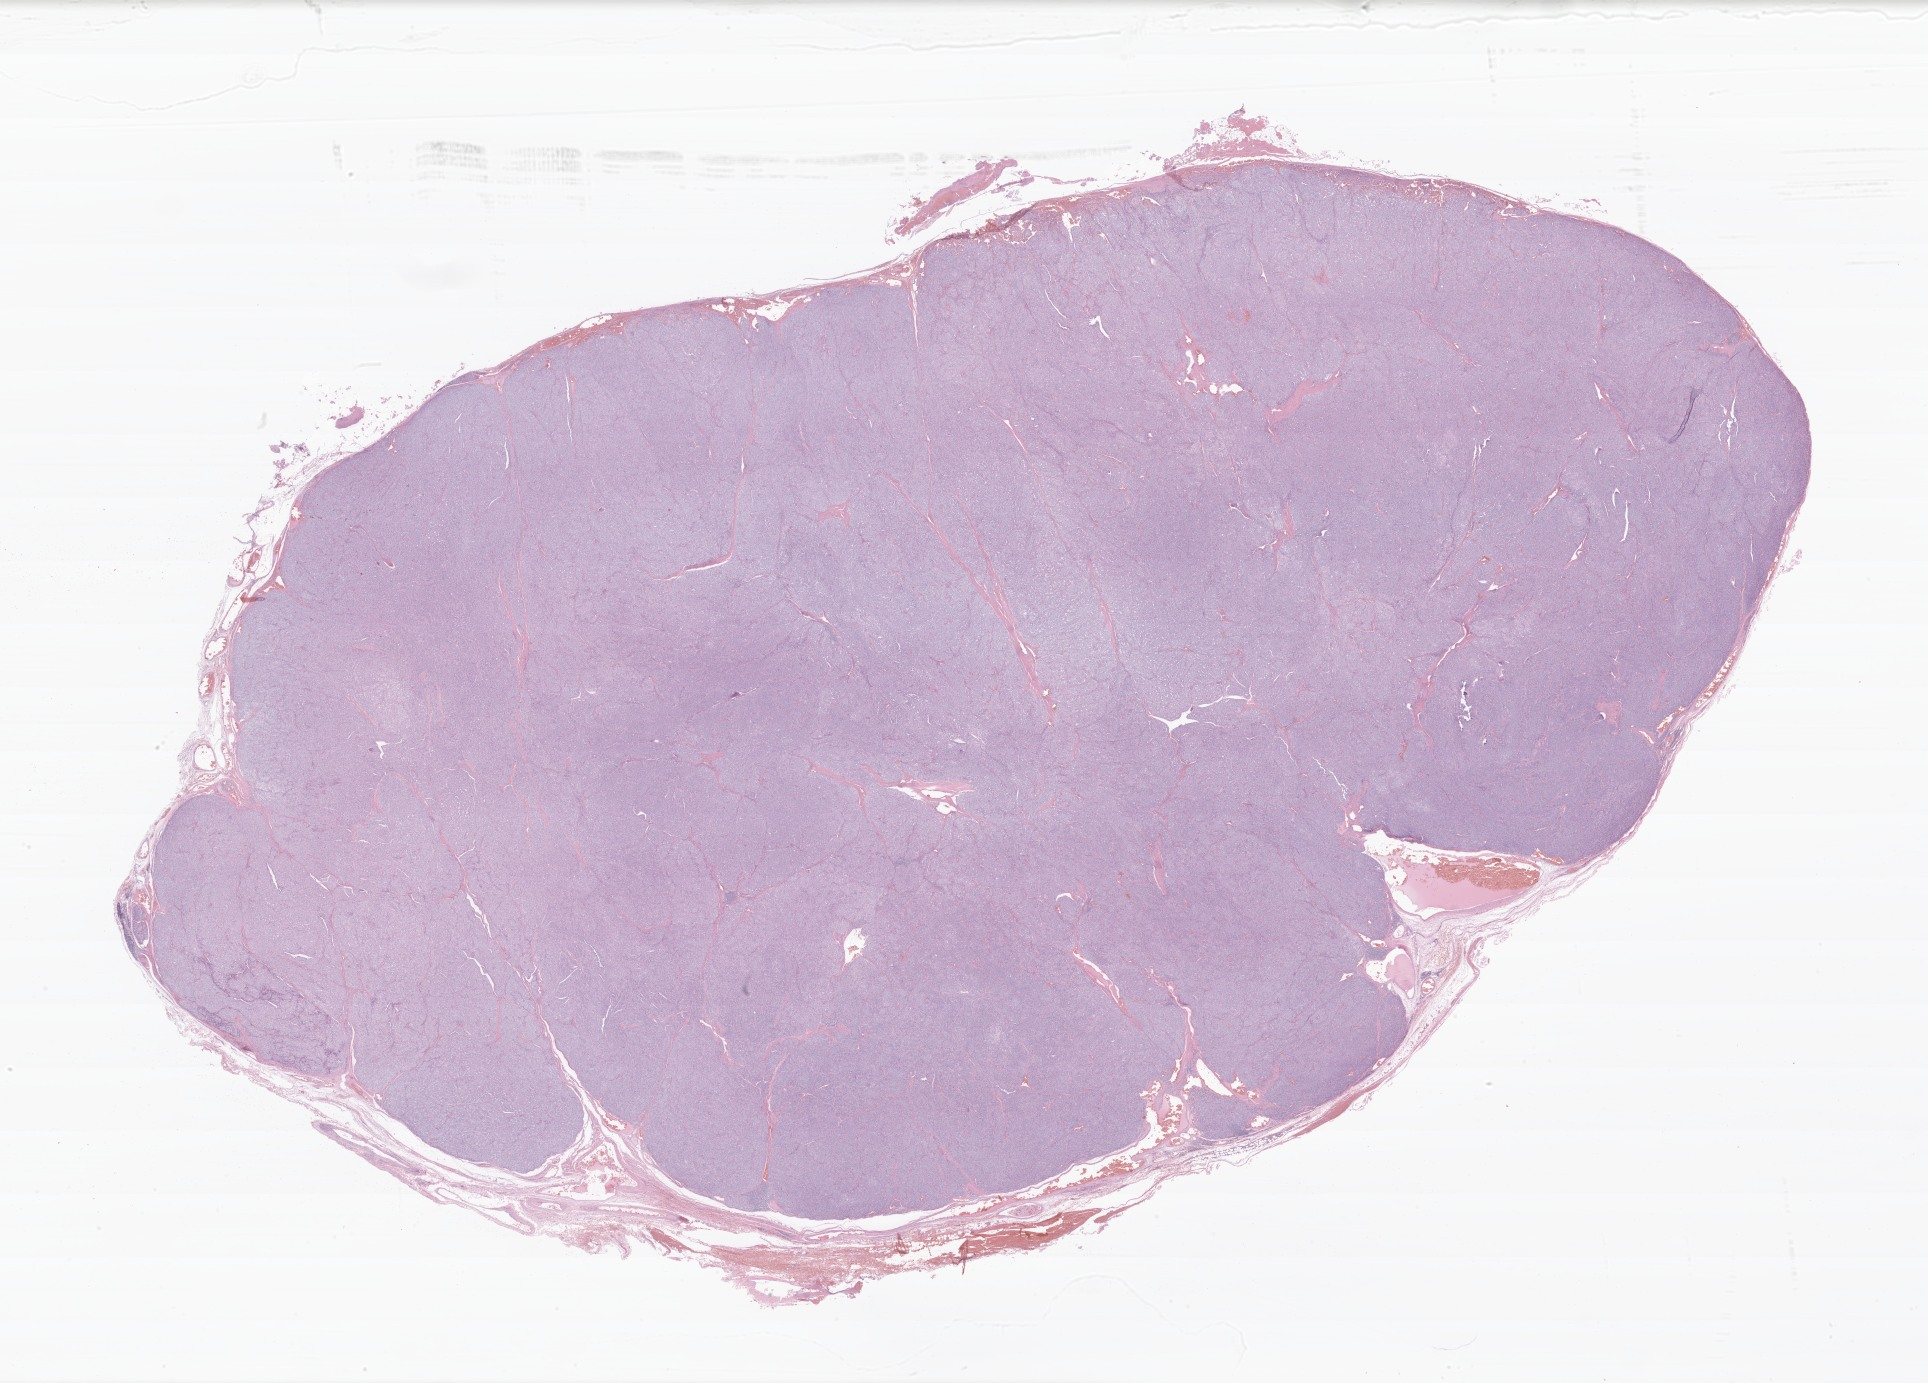
Digitized haematoxylin and eosin-stained section of tumor tissue from the thyroid, shown as a low-resolution overview of the whole scanned area (about 32.4 x 23.3 mm), FFPE section. Male patient, age 172 months (14 years 4 months).
Diagnosis (ICD-O-3 morphology term): Papillary carcinoma, NOS.